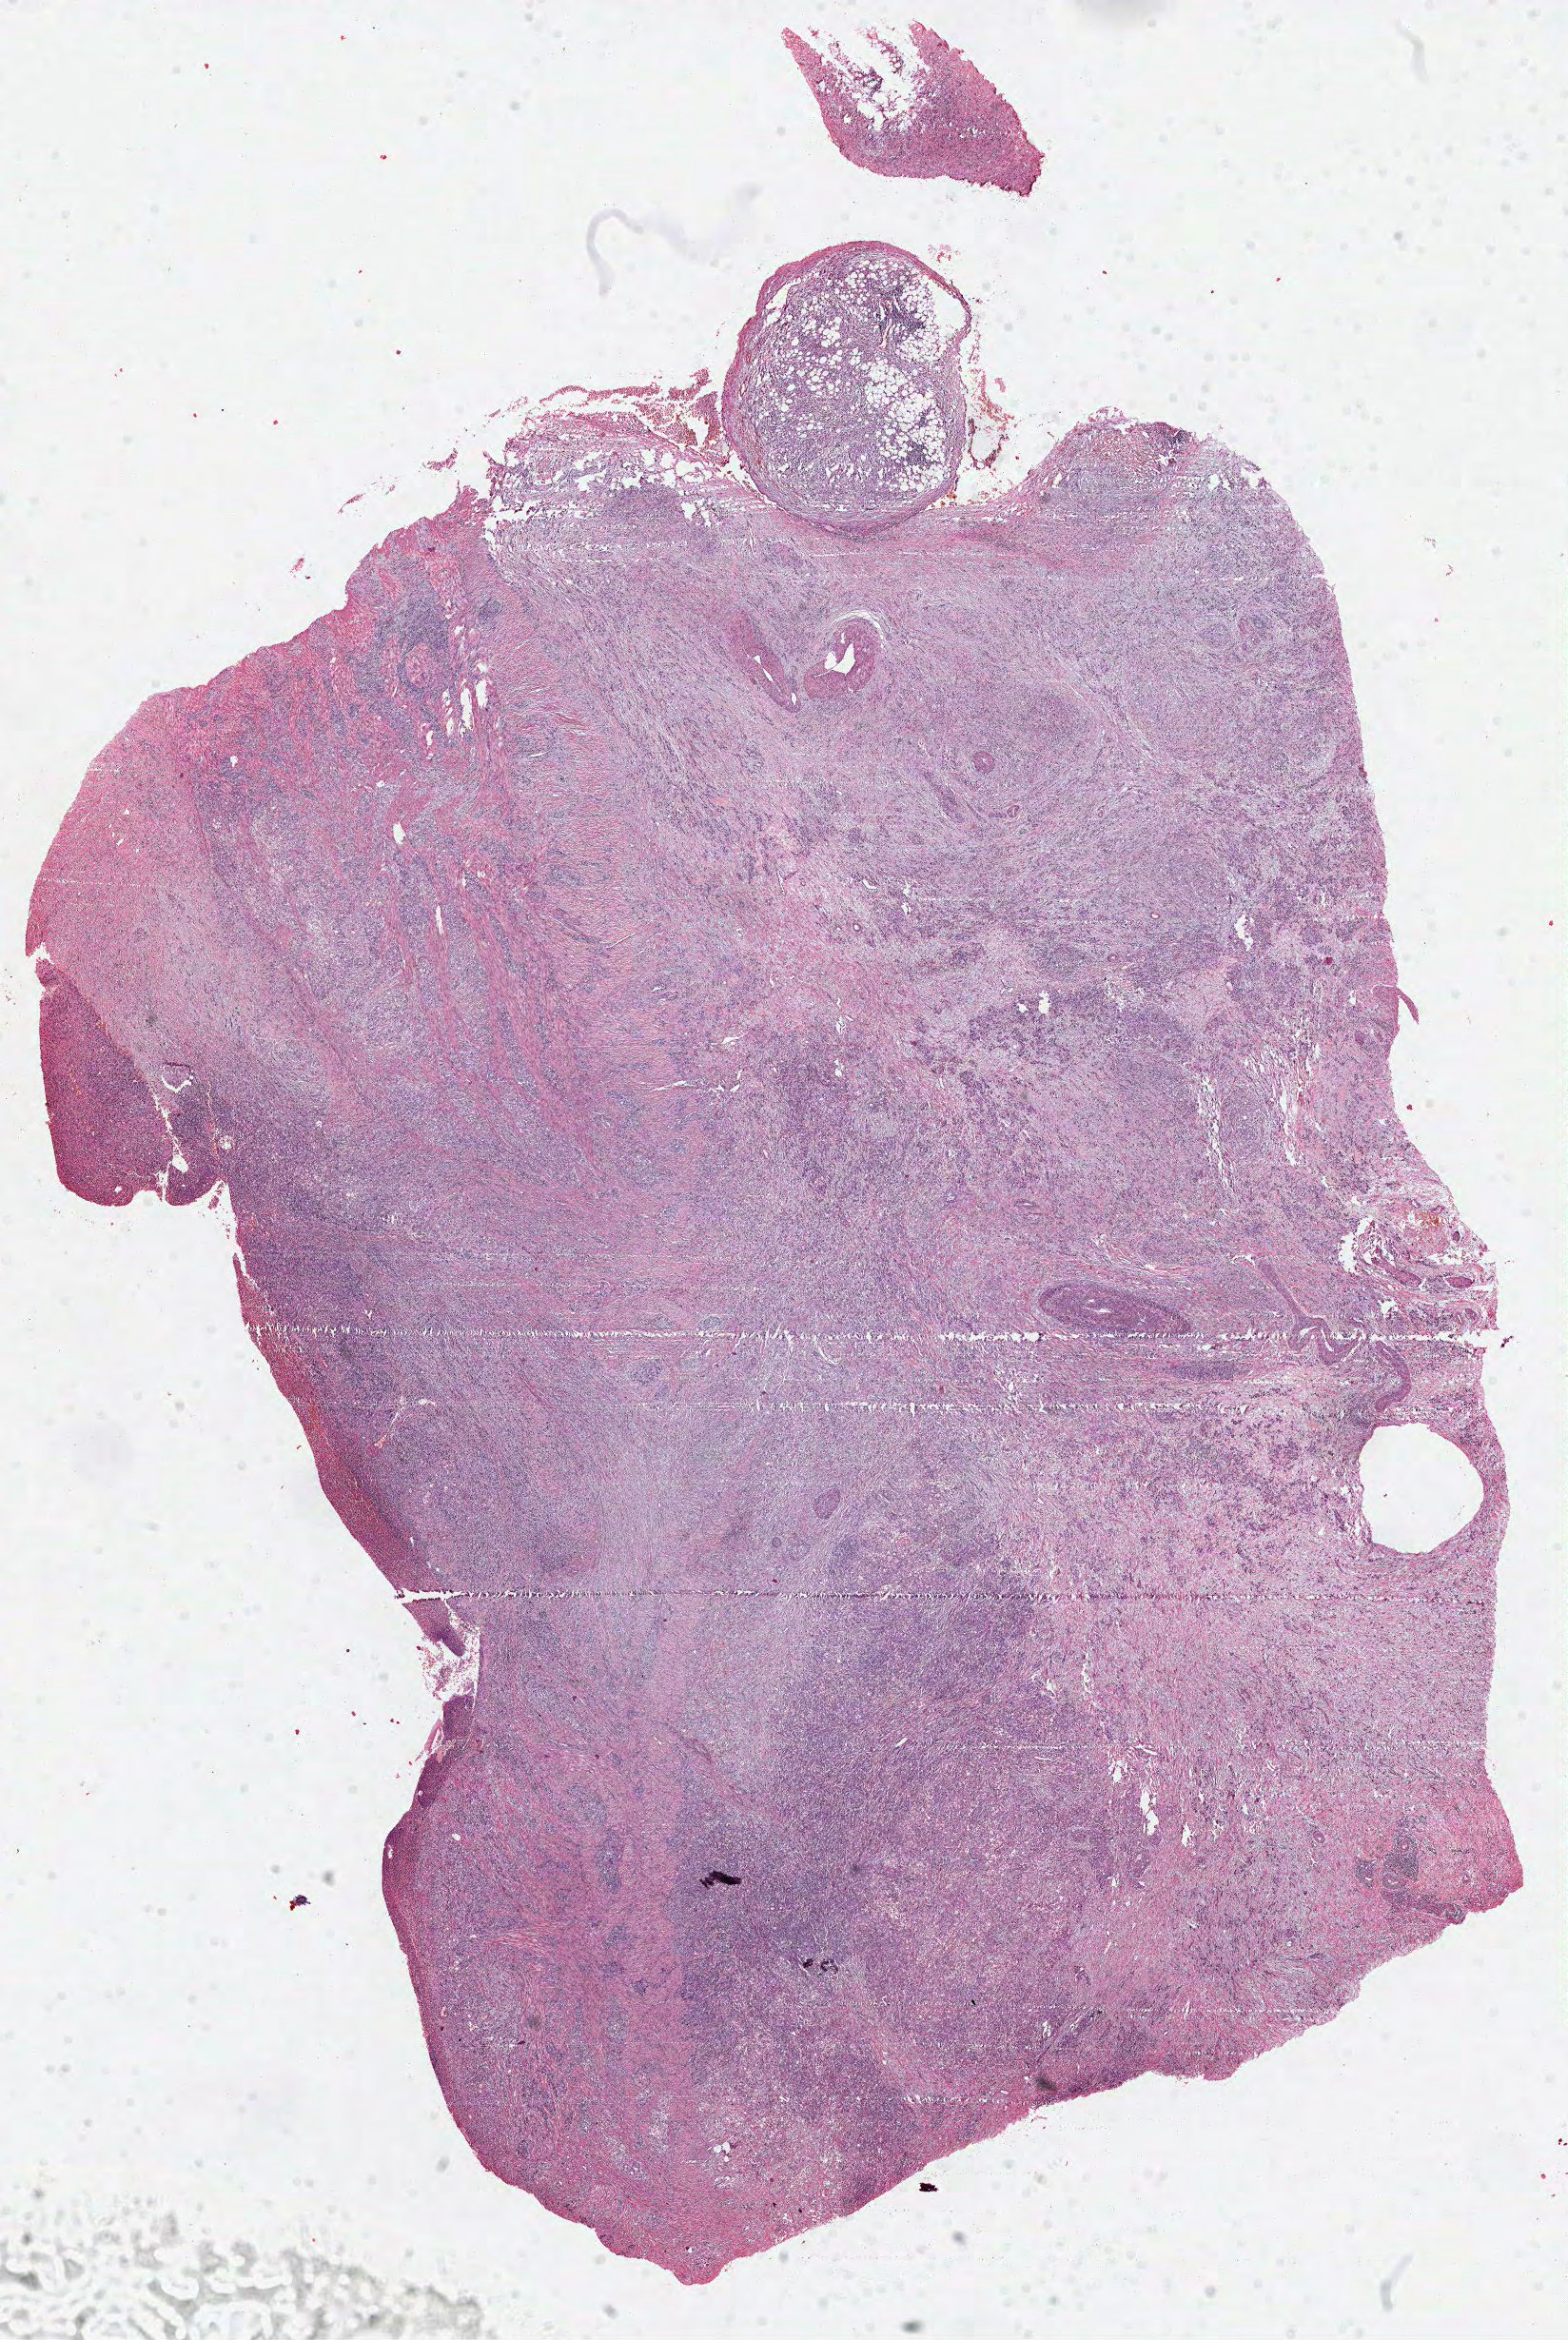
Digitized H&E-stained tissue section (whole slide), low-resolution overview of the scanned area, about 13.3 x 19.8 mm (from a 40x scan), FFPE section, sample: primary tumour, stomach. Male patient; age at initial diagnosis 45 years. Histologic grade: G3 (poorly differentiated).
AJCC pathologic stage: II (6th edition). Histologic diagnosis: Adenocarcinoma, intestinal type (gastric antrum).